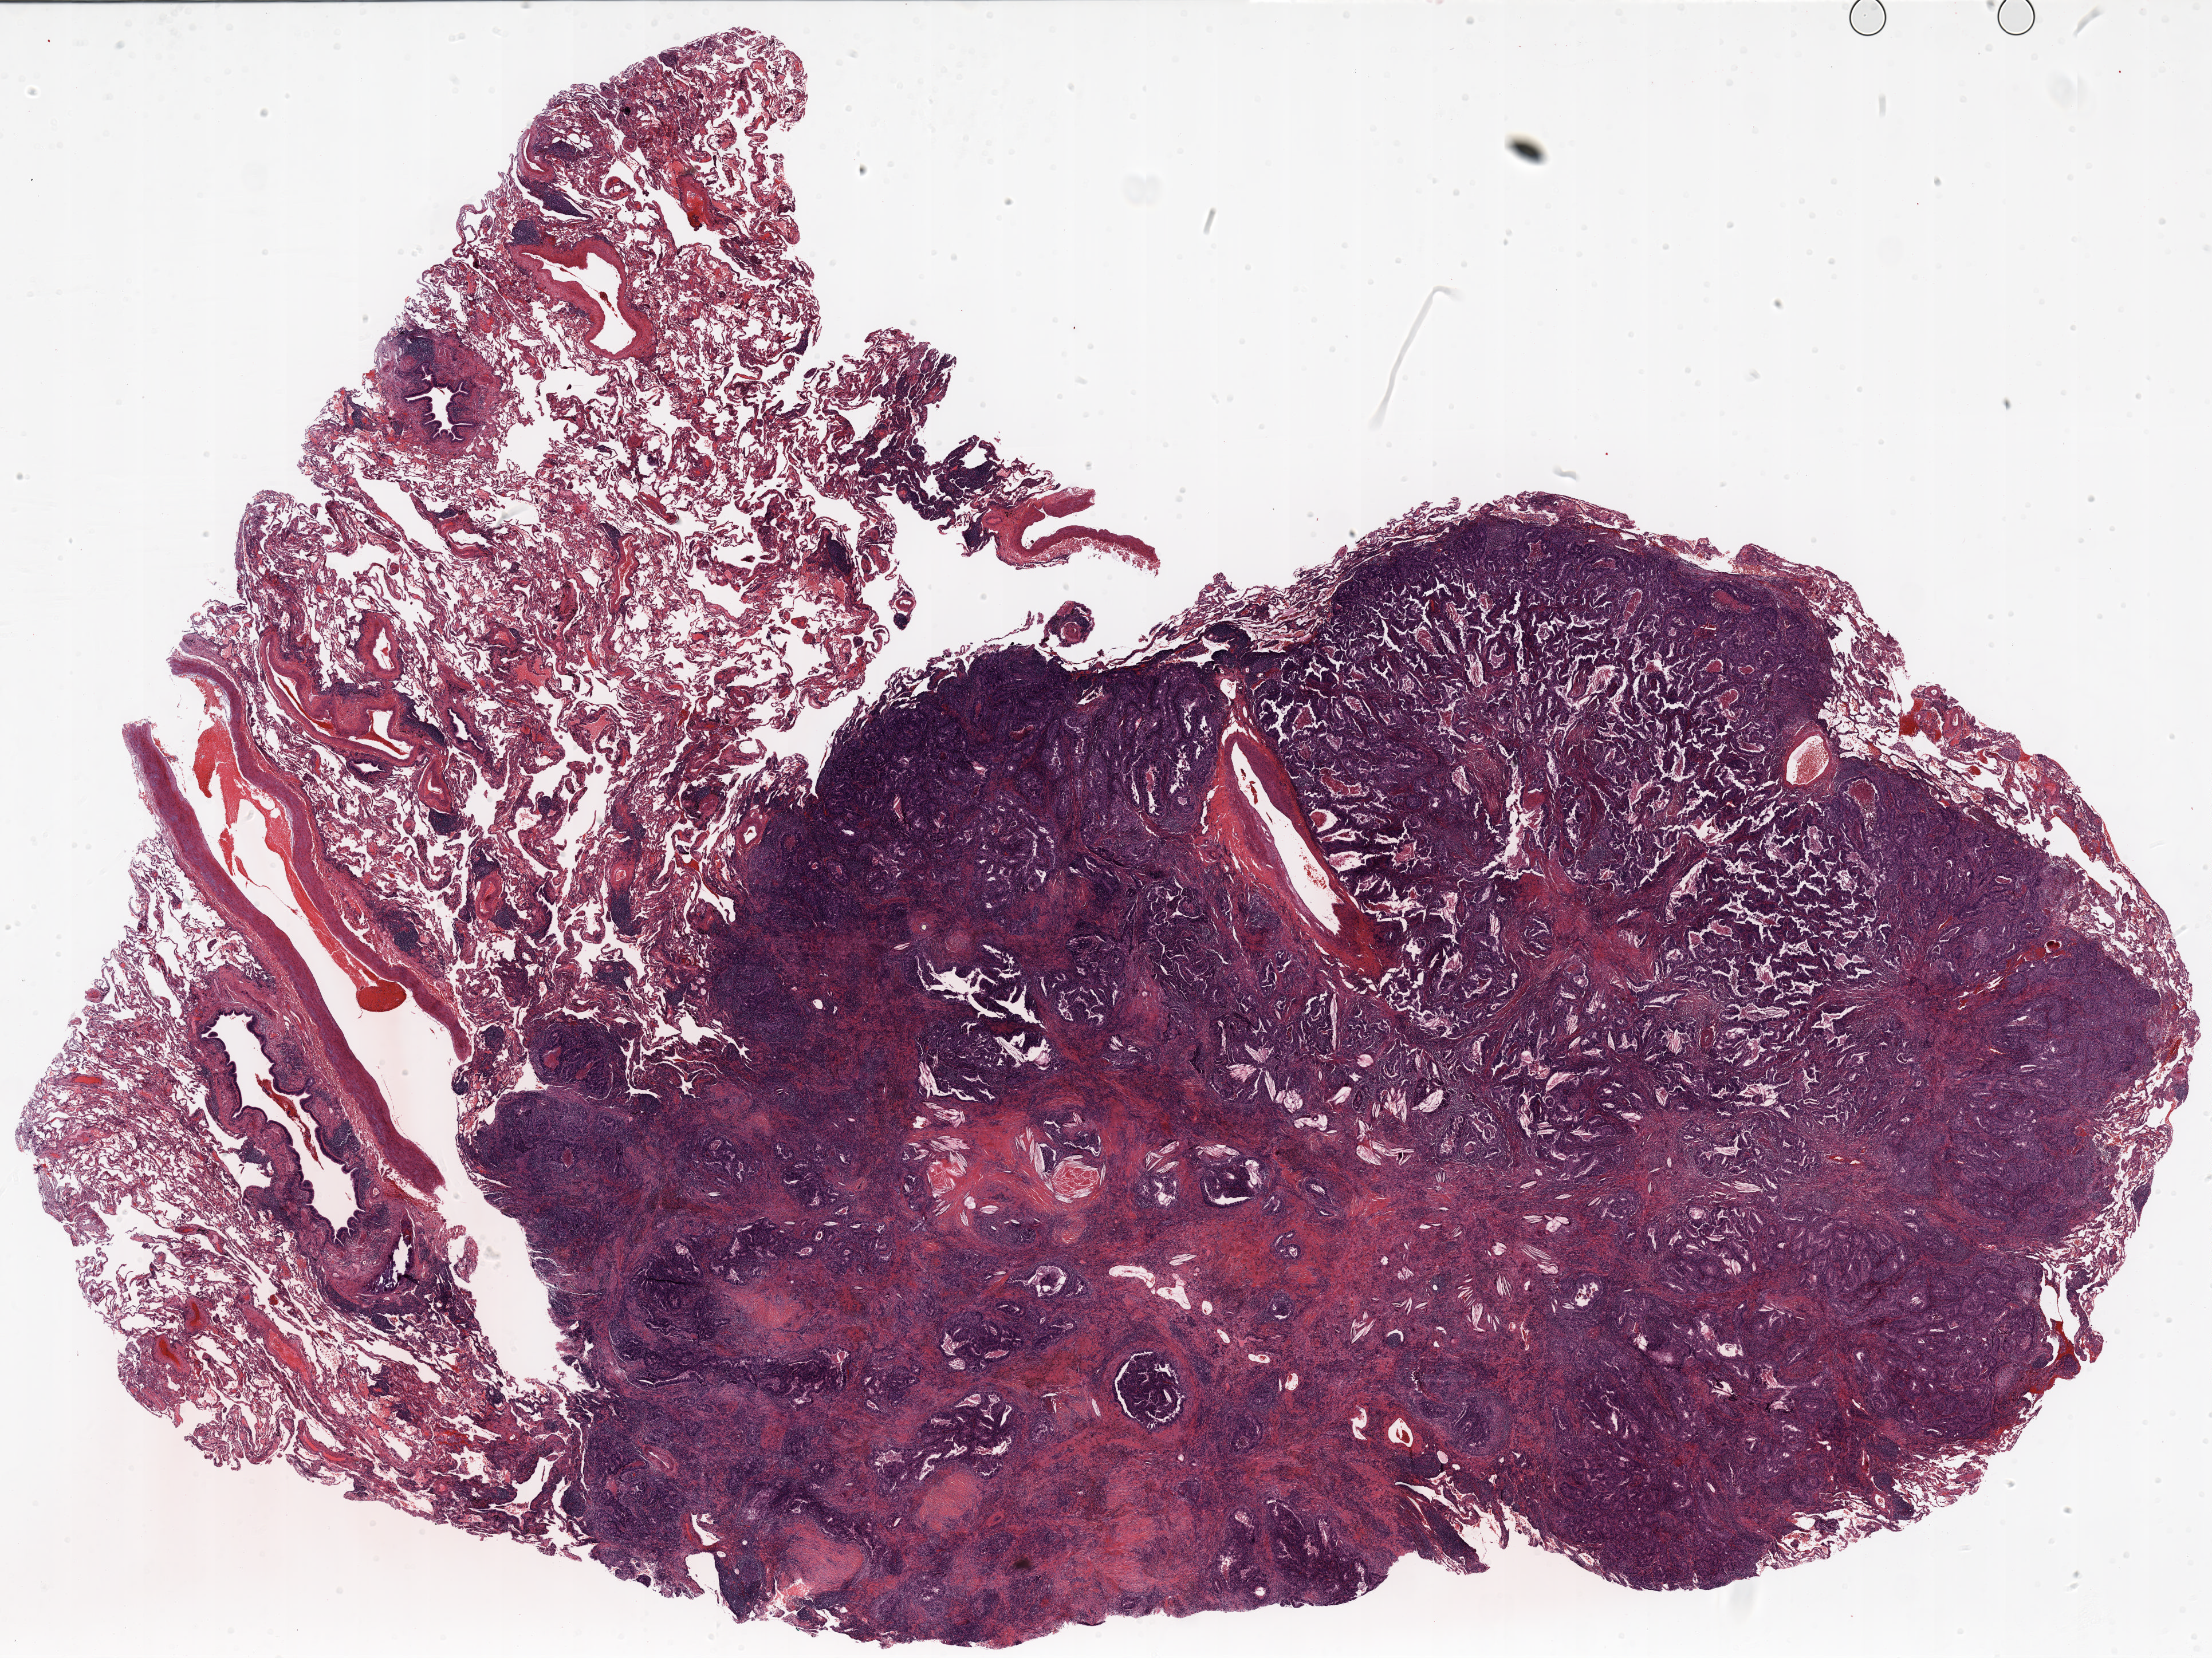
Hematoxylin and eosin (H&E) stained whole-slide image — low-resolution overview of the scanned area, about 31.0 x 23.3 mm (slide scanned at 20x); FFPE section; lung. Female patient, aged 72 at enrolment. Former smoker at enrolment. Grade: moderately differentiated (G2).
Stage (AJCC 6th edition): IA. Participant's lung-cancer diagnosis: Adenocarcinoma, NOS (ICD-O-3 8140/3). Primary tumour location (clinical record): left upper lobe. Tumour size (pathology): 25 mm. Note: participant had 2 primary lung cancers recorded; fields above describe the first.